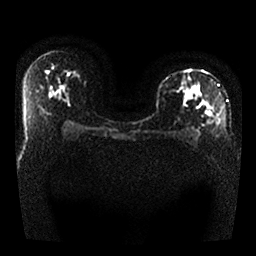
Breast MRI, one axial slice; position 16 of 25 along the scan axis; diffusion-weighted series; image 2 of 4 stored at this slice position (different b-values; order by instance number); 1.5 T; 4 mm slice thickness; 256 × 256 image matrix. Female patient.
Annotated regions visible in this slice (expert manual segmentation):
- tumour on diffusion-weighted imaging: bounding box [x1, y1, x2, y2] px = [185, 87, 215, 118]